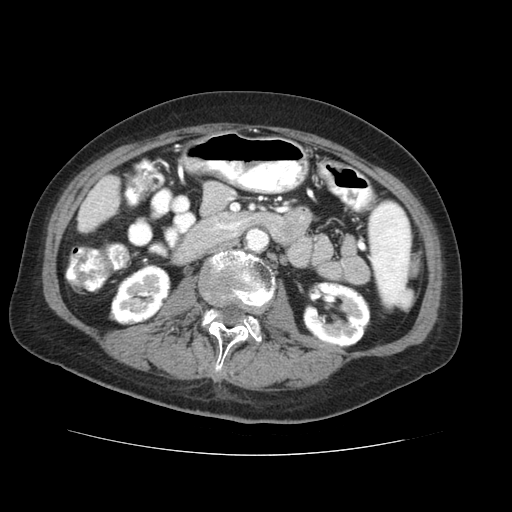
Contrast-enhanced abdominal CT (liver protocol), one axial slice. Position 5 of 73 along the scan axis. Reconstruction kernel STANDARD. 120 kVp. Soft-tissue window (W 400 / L 40 HU). 2.5 mm slice thickness. 512 × 512 image matrix, field of view 360 × 360 mm. From the clinical record (not read from this slice): diagnosis: hepatocellular carcinoma (patient treated with transarterial chemoembolisation; whether this scan precedes or follows treatment is not stated here); TNM stage (as recorded): Stage-IVB; Child-Pugh class: A.
Annotated regions visible in this slice (semi-automatically segmented with operator editing):
- liver parenchyma outside the tumour (the mass and vessels are separate outlines, so this box may not span the whole liver): bounding box (x1, y1, x2, y2) in pixels: (78, 175, 120, 232)
- liver vessels: (83, 203, 103, 226)